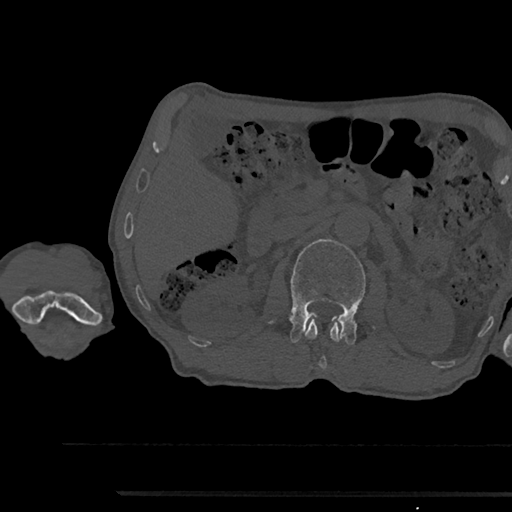
CT including the spine, one axial slice. Slice 592 of 797 in the series (ordered by position). 120 kVp. Bone window (W 1800 / L 400 HU). 0.5 mm slice thickness. 512 × 512 image matrix. Male patient, age 79 years. Case-level facts recorded for this patient, not image findings: primary cancer: prostate.
Outlined on this slice (semi-automatically segmented with operator editing):
- L1 vertebra: bounding box (x1, y1, x2, y2) in pixels: (305, 319, 341, 368)
- L2 vertebra: (289, 239, 366, 345)